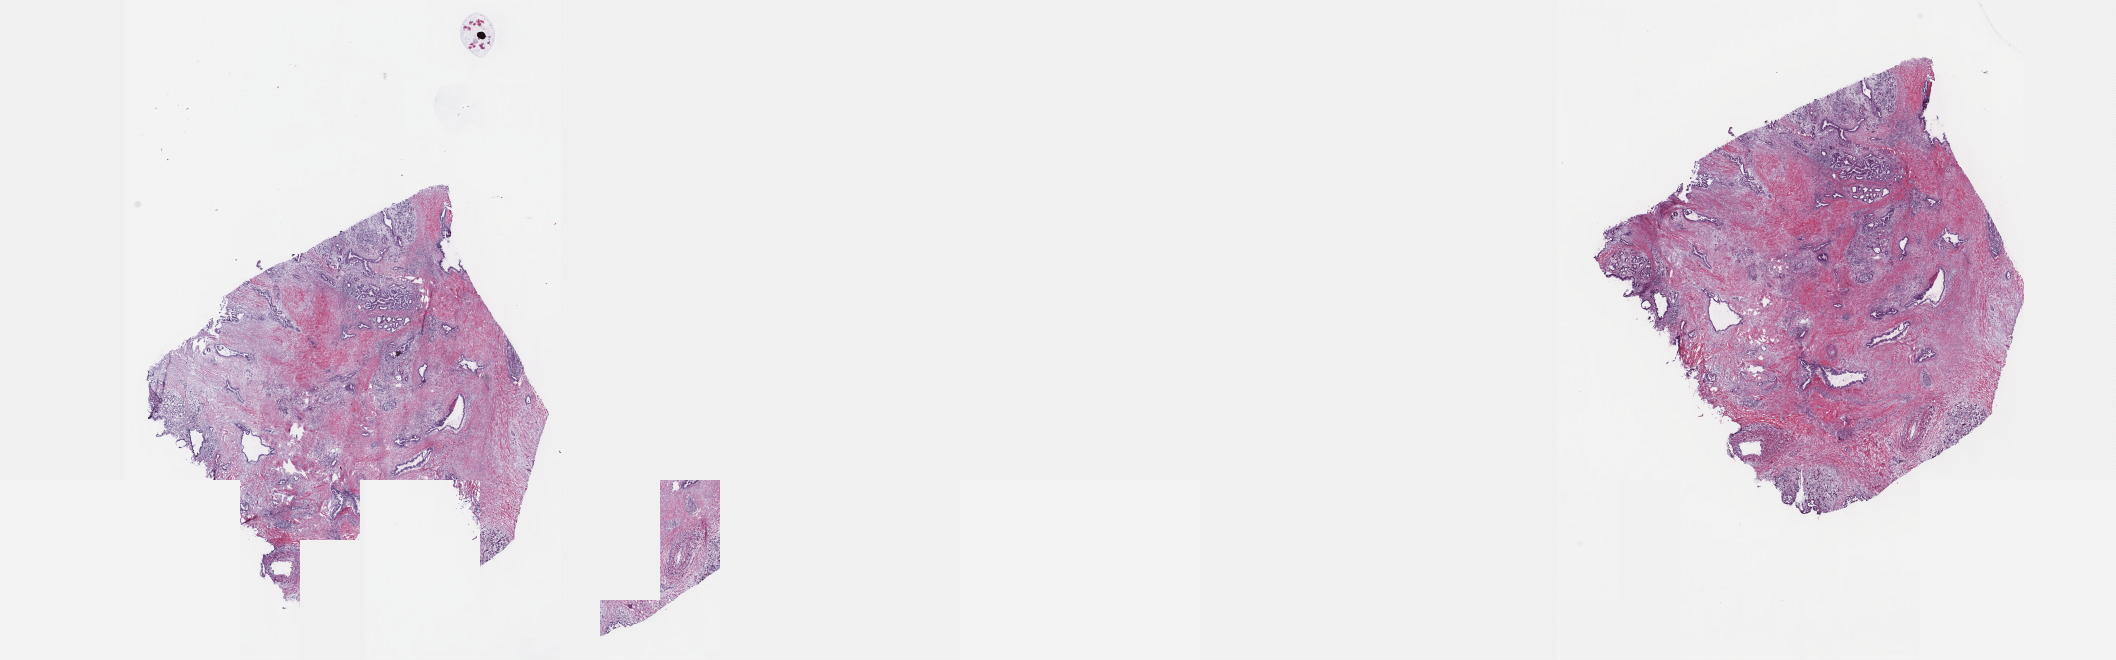
Digitized Hematoxylin and eosin (H&E) stained tissue section (whole slide) — shown as a low-resolution overview of the whole scanned area (about 34.2 x 10.7 mm, acquisition: 40x scan). Frozen section from the top of the tissue portion. Sample: primary tumour, pancreas. Male, age 65 years at initial diagnosis. Histologic grade: G3 (poorly differentiated). Composition of this section per pathologist review: tumour cells 40%, tumour nuclei 40%, normal cells 40%, stromal cells 20%, necrosis 0%. Infiltration values recorded for this section: lymphocyte infiltration 40%, monocyte infiltration 20%, neutrophil infiltration 20%.
Lymph nodes positive (case pathology): 7 of 22 examined. TNM: T3 N1 M0. AJCC pathologic stage: IIB. Histologic diagnosis: Mucinous adenocarcinoma (head of pancreas).